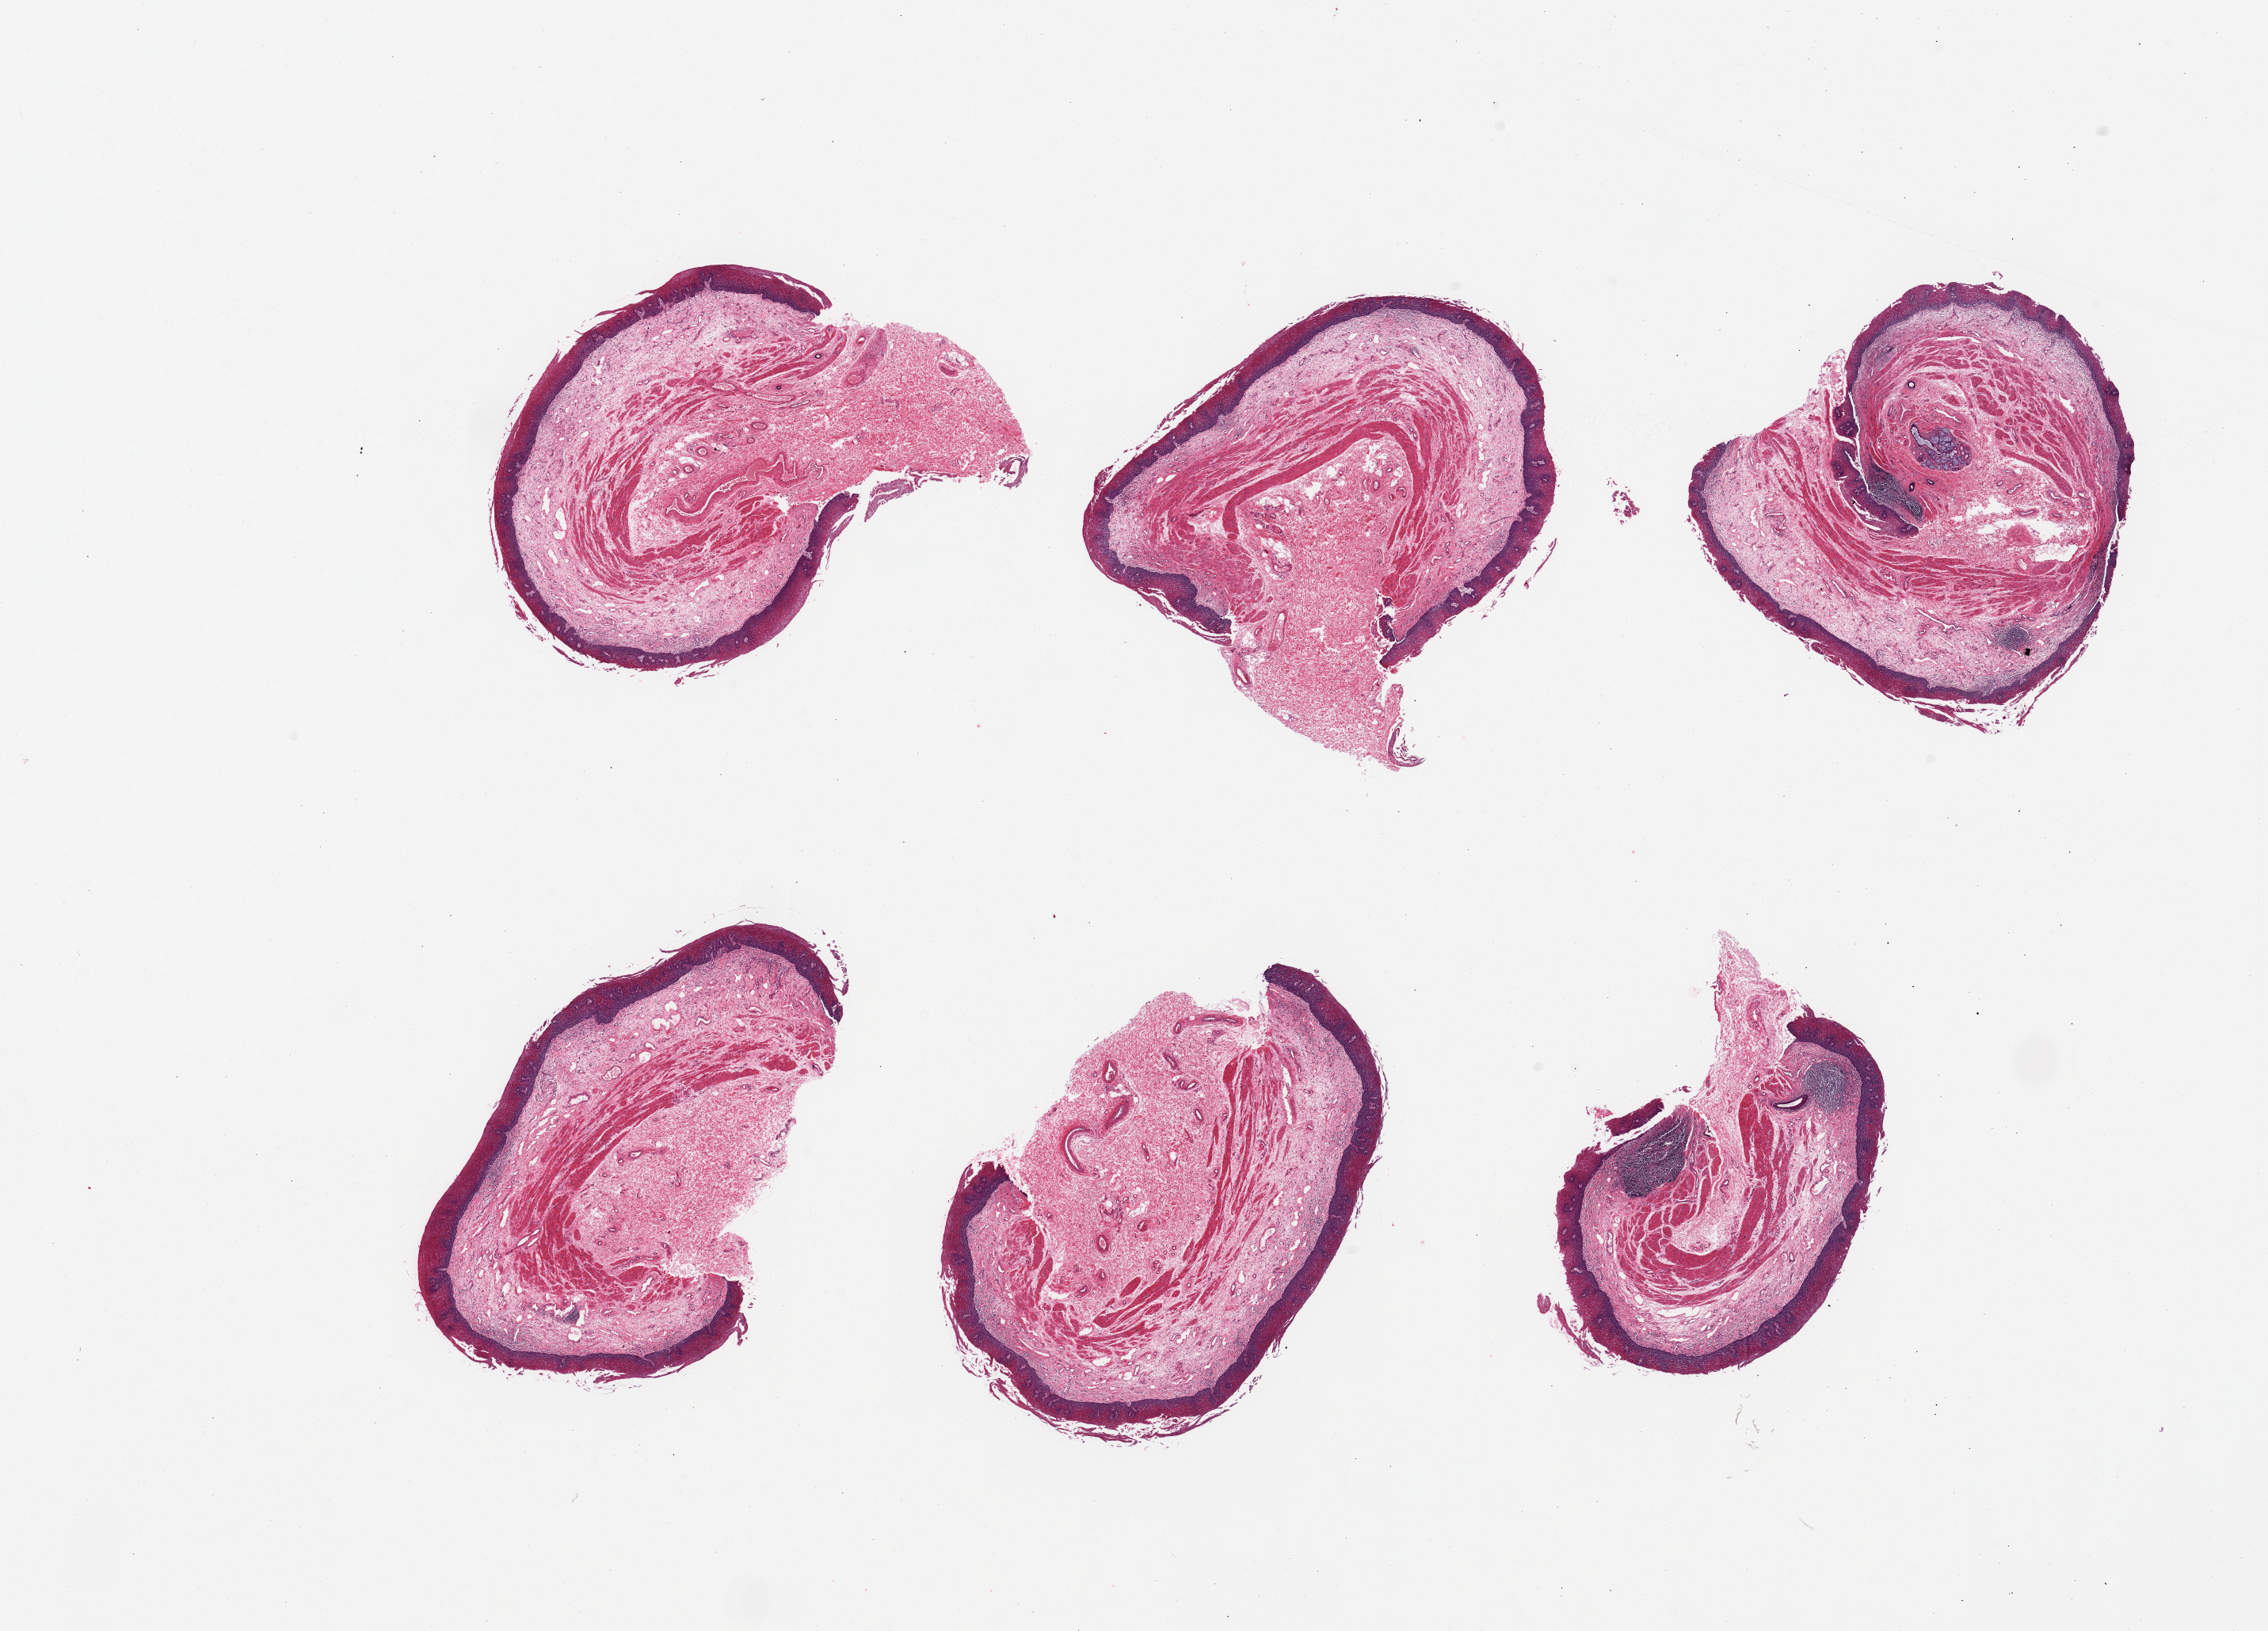
Whole-slide image, hematoxylin and eosin (H&E) stain, whole scanned area (about 22.6 x 16.3 mm) shown as a low-resolution overview, PAXgene-fixed paraffin-embedded (PFPE) section, target tissue: esophageal mucous membrane, tissue donor sample. Donor: male.
• reviewer comment on this tissue sample: 6 pieces; focal desquamation of the surface; ~0.3mm thick squamous epithelium; submucosa with focal lymphoid aggregates; submucosal gland